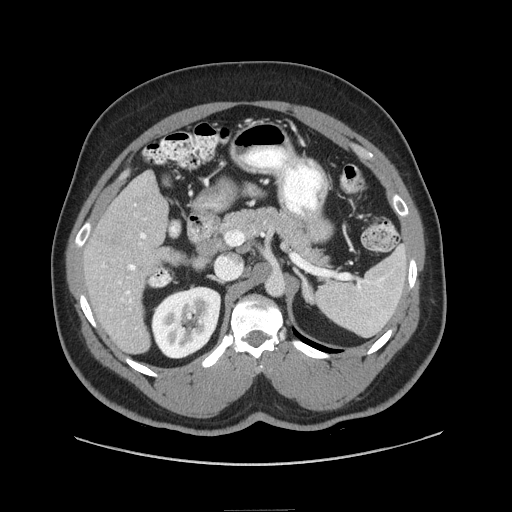
Contrast-enhanced abdominal CT (liver protocol), one axial slice; position 39 of 87 along the scan axis; soft-tissue window (W 400 / L 40 HU); 2.5 mm slice thickness; 512 × 512 image matrix, field of view 440 × 440 mm. From the clinical record (not read from this slice): diagnosis: hepatocellular carcinoma (patient treated with transarterial chemoembolisation; whether this scan precedes or follows treatment is not stated here); TNM stage (as recorded): Stage-II; Child-Pugh class: A; tumour differentiation: moderately differentiated.
Annotated regions visible in this slice (semi-automatically segmented with operator editing):
- liver parenchyma outside the tumour (the mass and vessels are separate outlines, so this box may not span the whole liver): bounding box <84,170,178,352> (left, top, right, bottom; pixels)
- liver vessels: <101,204,146,303>